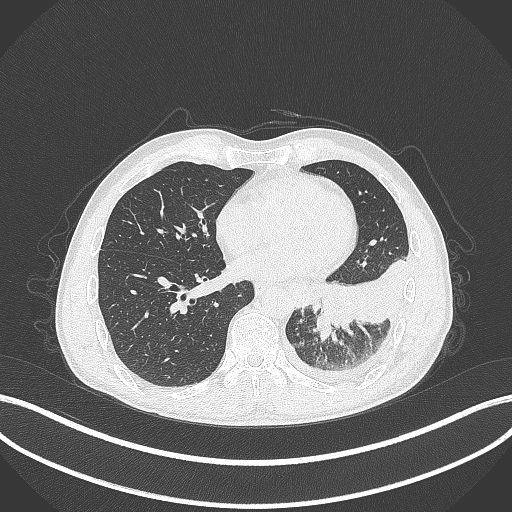
Chest CT, one axial slice. Slice 112 of 295 in the series (ordered by position). Reconstruction kernel B70f. 120 kVp. Lung window (W 1500 / L -600 HU). 1 mm slice thickness. 512 × 512 image matrix. Male patient, age 47 years. From the clinical record (not read from this slice): clinical TNM (as recorded): T3 N1 M1c; histopathological grade: G3.
Annotated regions visible in this slice (rectangle marked by the reading radiologist):
- lung tumour (recorded histology: small cell carcinoma): bounding box <313,313,333,342> (left, top, right, bottom; pixels)